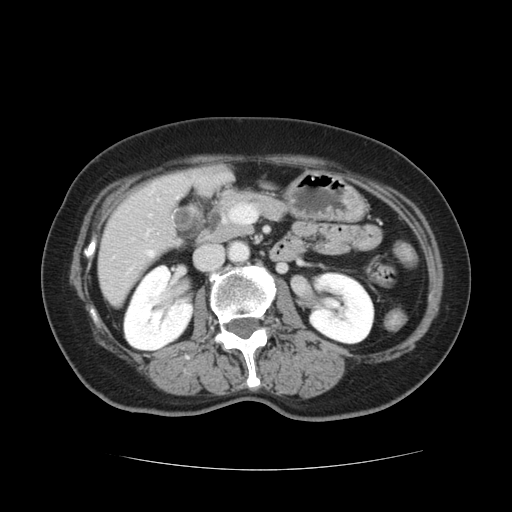
Contrast-enhanced abdominal CT, one axial slice; position 46 of 128 along the scan axis; intravenous contrast given; soft-tissue window (W 400 / L 40 HU); 2.5 mm slice thickness; 512 × 512 image matrix, field of view 366 × 366 mm. Female patient, age 67 years. From the clinical record (not read from this slice): diagnosis: colorectal cancer liver metastases, imaged before liver resection.
Structures marked on this image (manually delineated by an expert):
- hepatic veins: bounding box <149,252,153,254> (left, top, right, bottom; pixels)
- liver: <100,166,230,305>
- planned liver remnant (the part of the liver to remain after resection): <100,221,175,304>